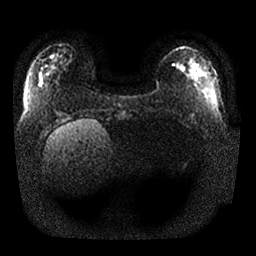
Breast MRI, one axial slice. Position 5 of 25 along the scan axis. Diffusion-weighted series; image 2 of 4 stored at this slice position (different b-values; order by instance number). 1.5 T. 256 × 256 image matrix, field of view 350 × 350 mm. Female patient.
Outlined on this slice (outlined manually by an expert reader):
- tumour on diffusion-weighted imaging: bounding box (x1, y1, x2, y2) in pixels: (181, 66, 184, 70)